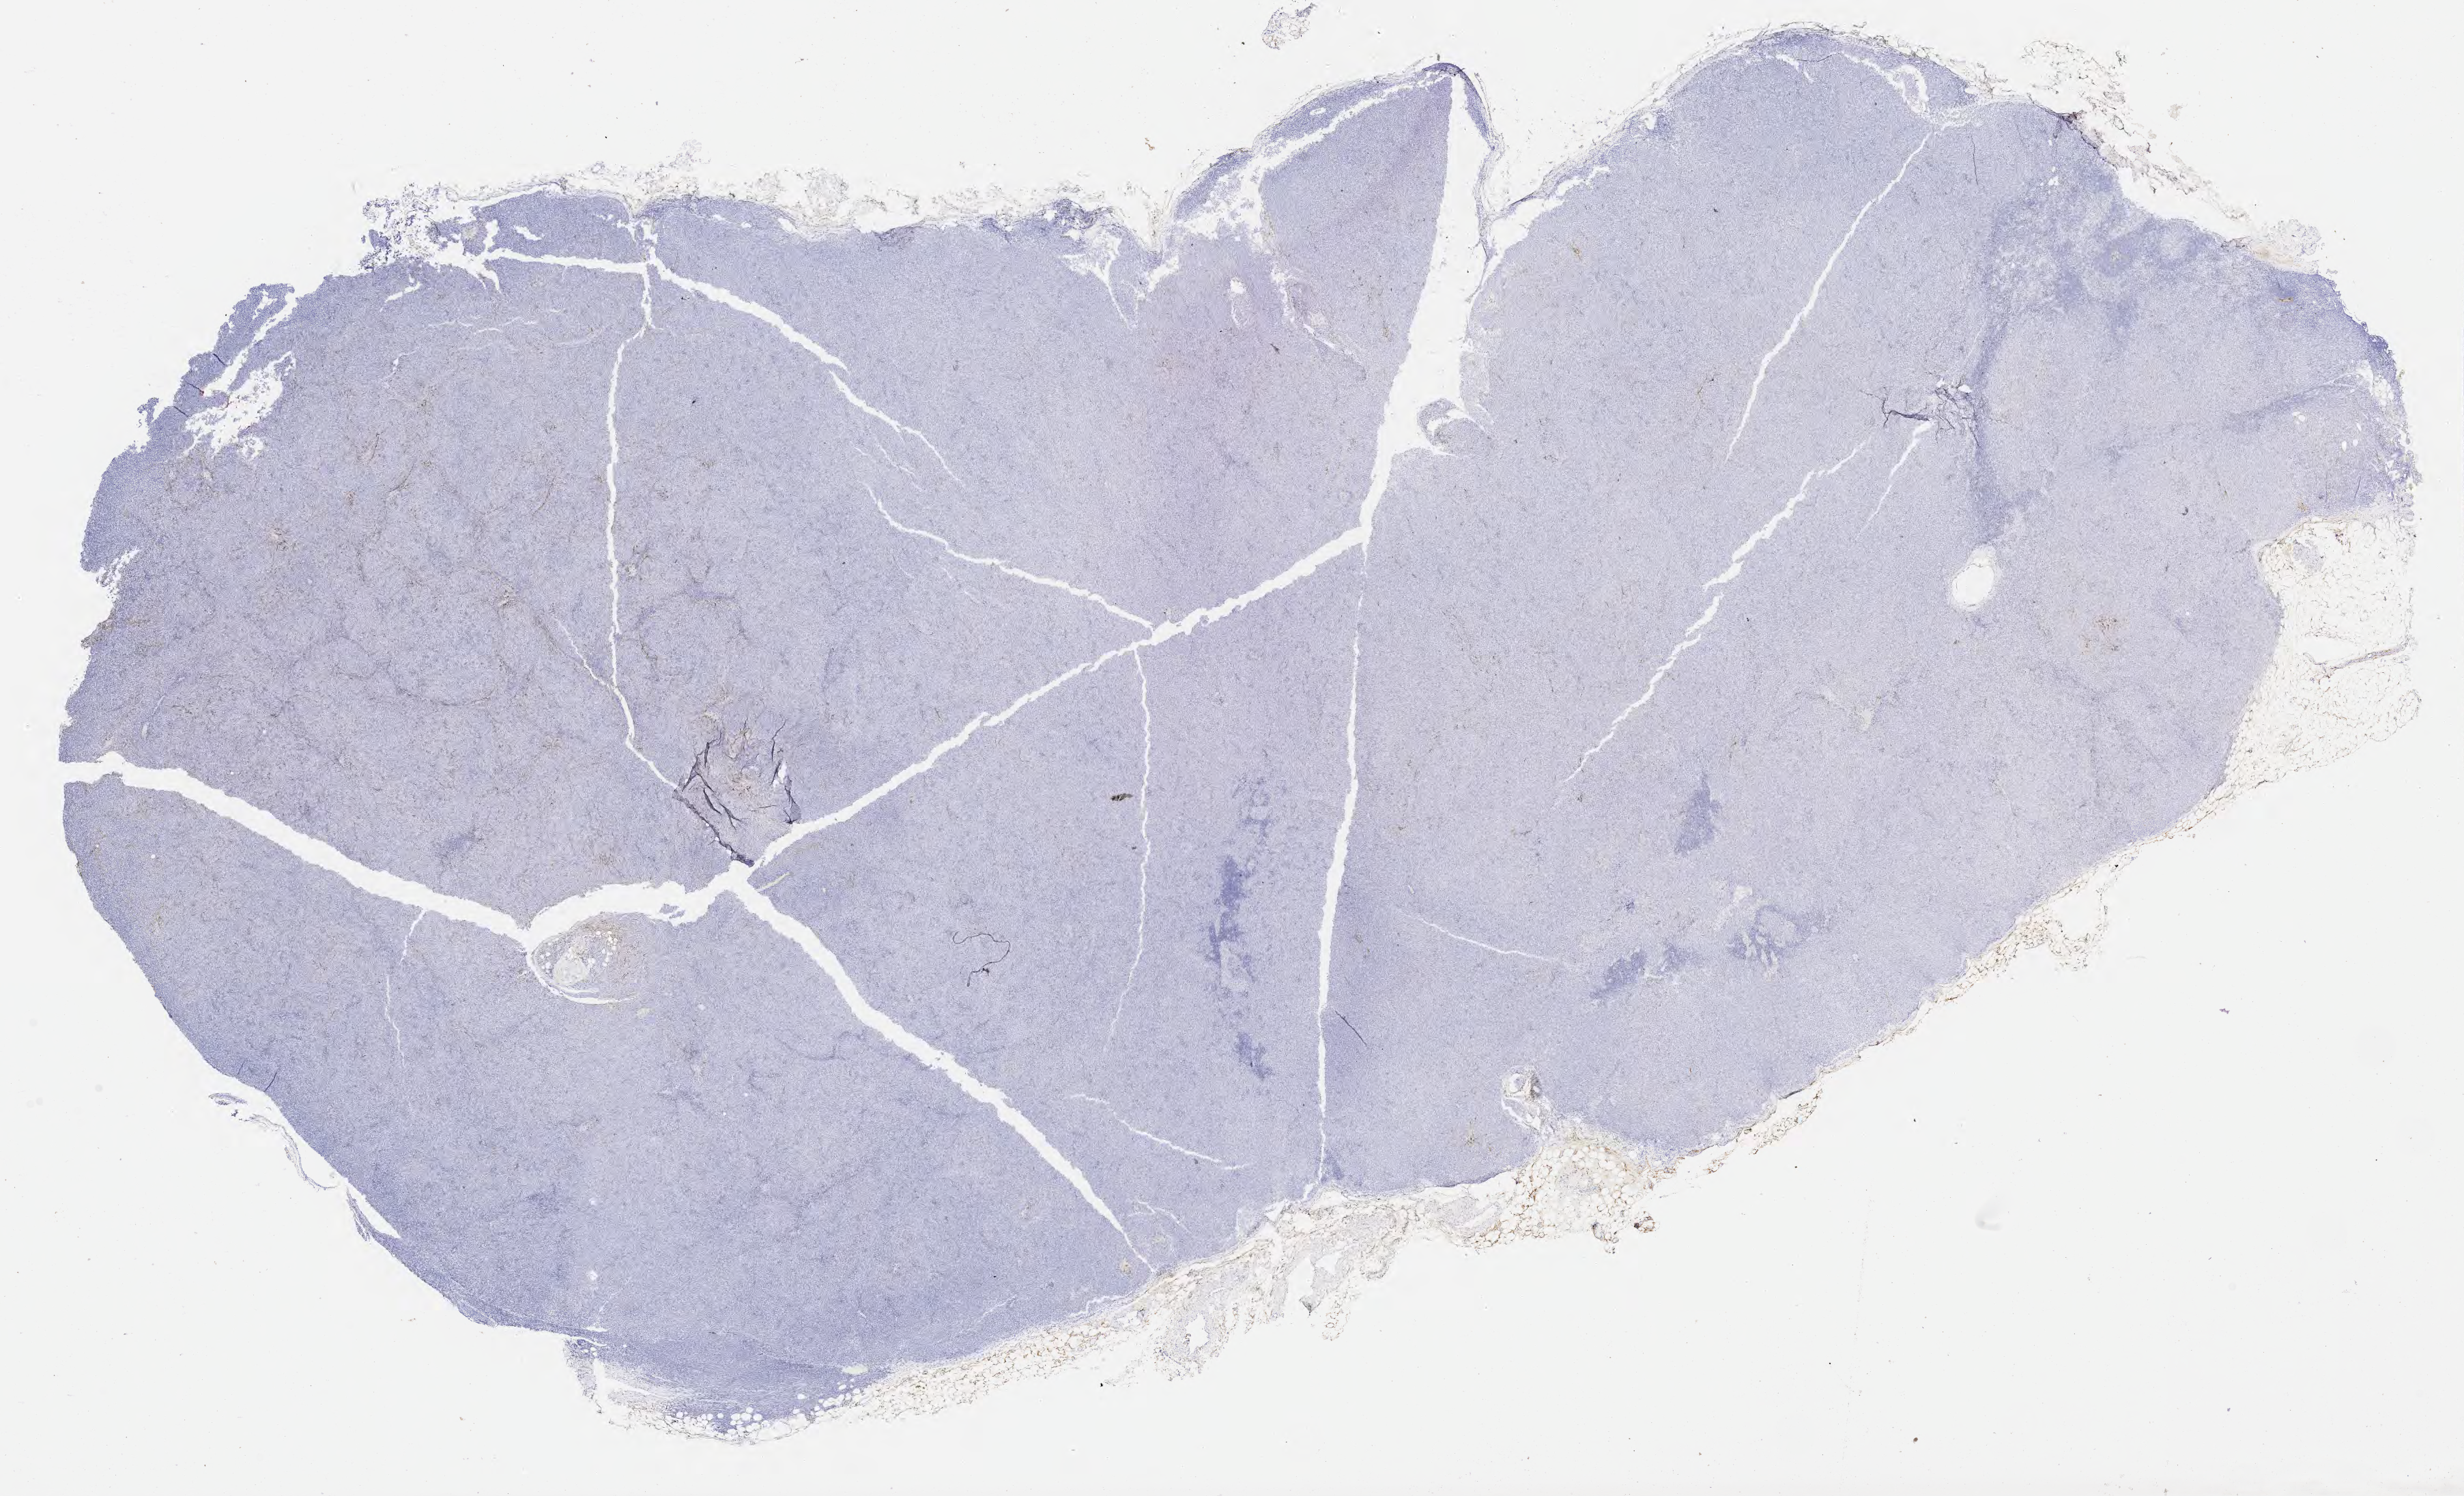
Whole-slide image, immunohistochemical stain for CD10 — low-resolution overview of the scanned area, about 29.2 x 17.7 mm. Tumor tissue. Patient: male, age 69 years.
Diagnosis: Diffuse large B-cell lymphoma, NOS.